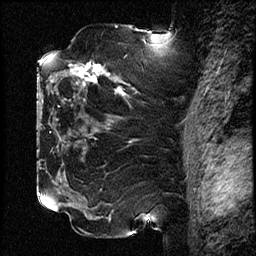
Breast MRI (dynamic contrast-enhanced), one sagittal slice; dynamic contrast-enhanced study with each time point stored as its own series, time point 2 of 3 at this slice position (early post-contrast, ordered by acquisition time); 1.5 T; TE 4.2 ms, TR 17.6 ms; 2 mm slice thickness; 256 × 256 image matrix, field of view 200 × 200 mm. Patient: female, 42 years. Case-level facts recorded for this patient, not image findings: setting: breast cancer imaged before/during neoadjuvant chemotherapy; receptor status: HER2-positive.
Outlined on this slice (semi-automatically segmented with operator editing):
- analysis volume of interest (the breast-tissue region the enhancement analysis was run in; not a lesion): bounding box [x1, y1, x2, y2] px = [50, 51, 129, 129]
- tumour enhancement mask (voxels above the 100 % enhancement threshold inside the analysis volume of interest): [70, 63, 124, 96]